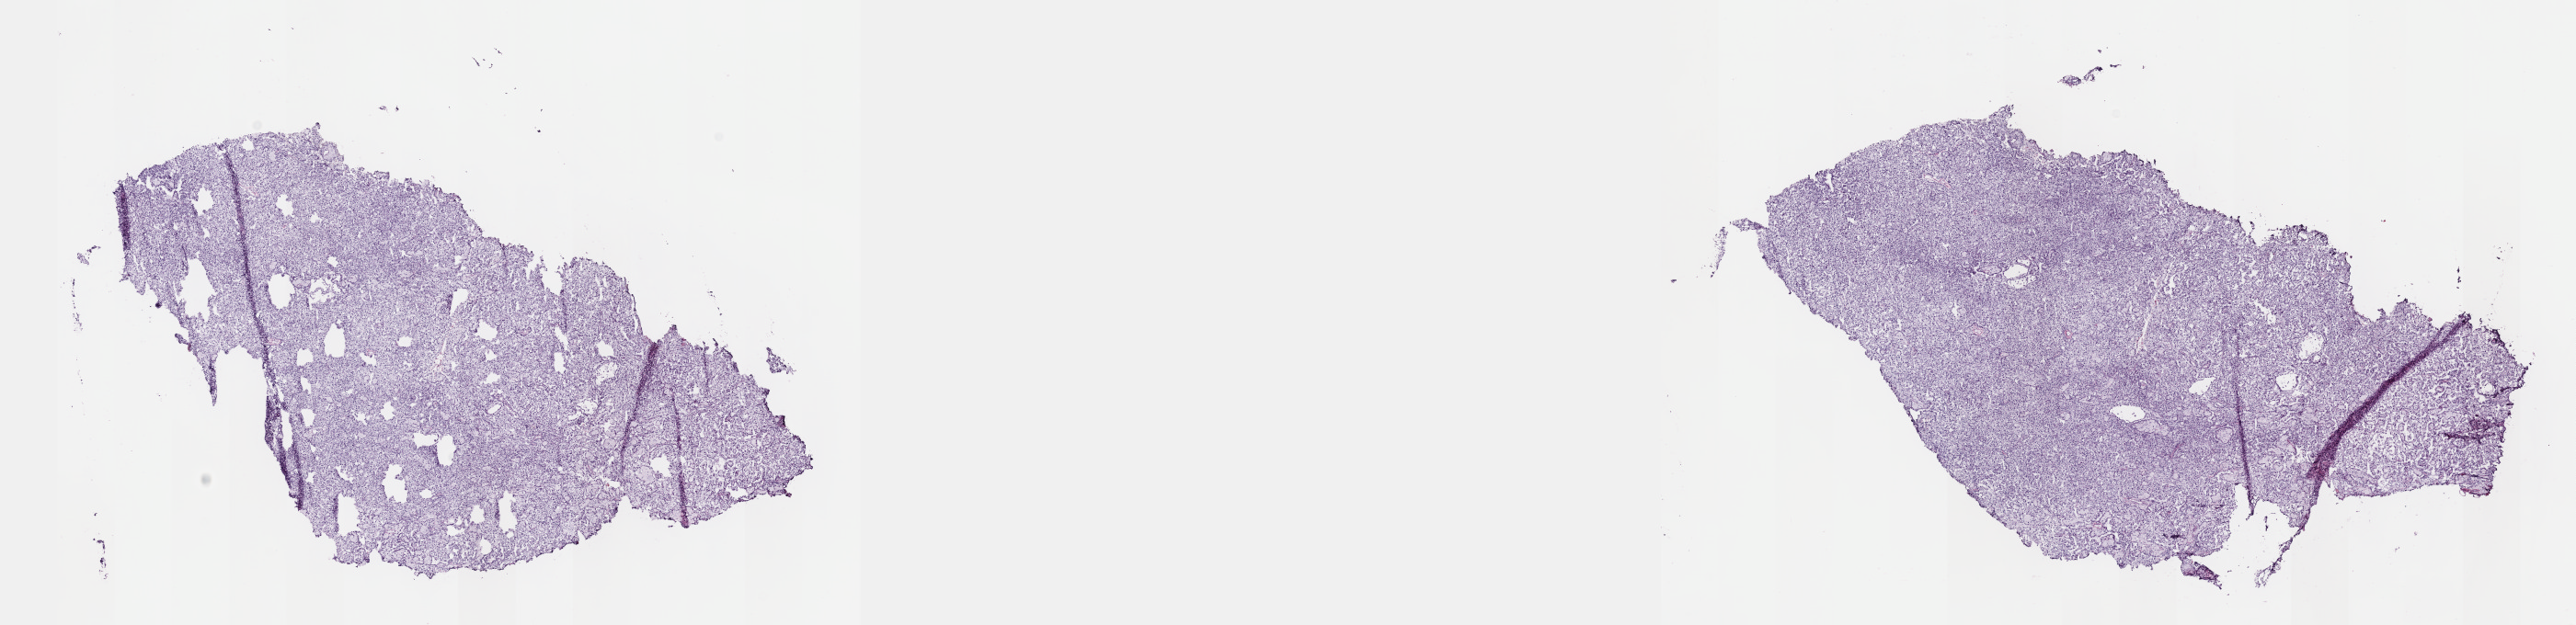
Whole-slide histology image, H&E — shown as a low-resolution overview of the whole scanned area (about 22.6 x 5.5 mm, slide scanned at 40x); frozen section from the top of the tissue portion; primary tumour sample from the kidney. Male, age 77 years at initial diagnosis. Slide review estimates, as recorded: tumour cells 90%, tumour nuclei 95%, normal cells 0%, stromal cells 10%, necrosis 0%. Inflammatory infiltration, as recorded: lymphocyte infiltration 0%, monocyte infiltration 0%, neutrophil infiltration 0%.
Diagnosis: Papillary adenocarcinoma, NOS. AJCC pathologic stage: I (6th edition).